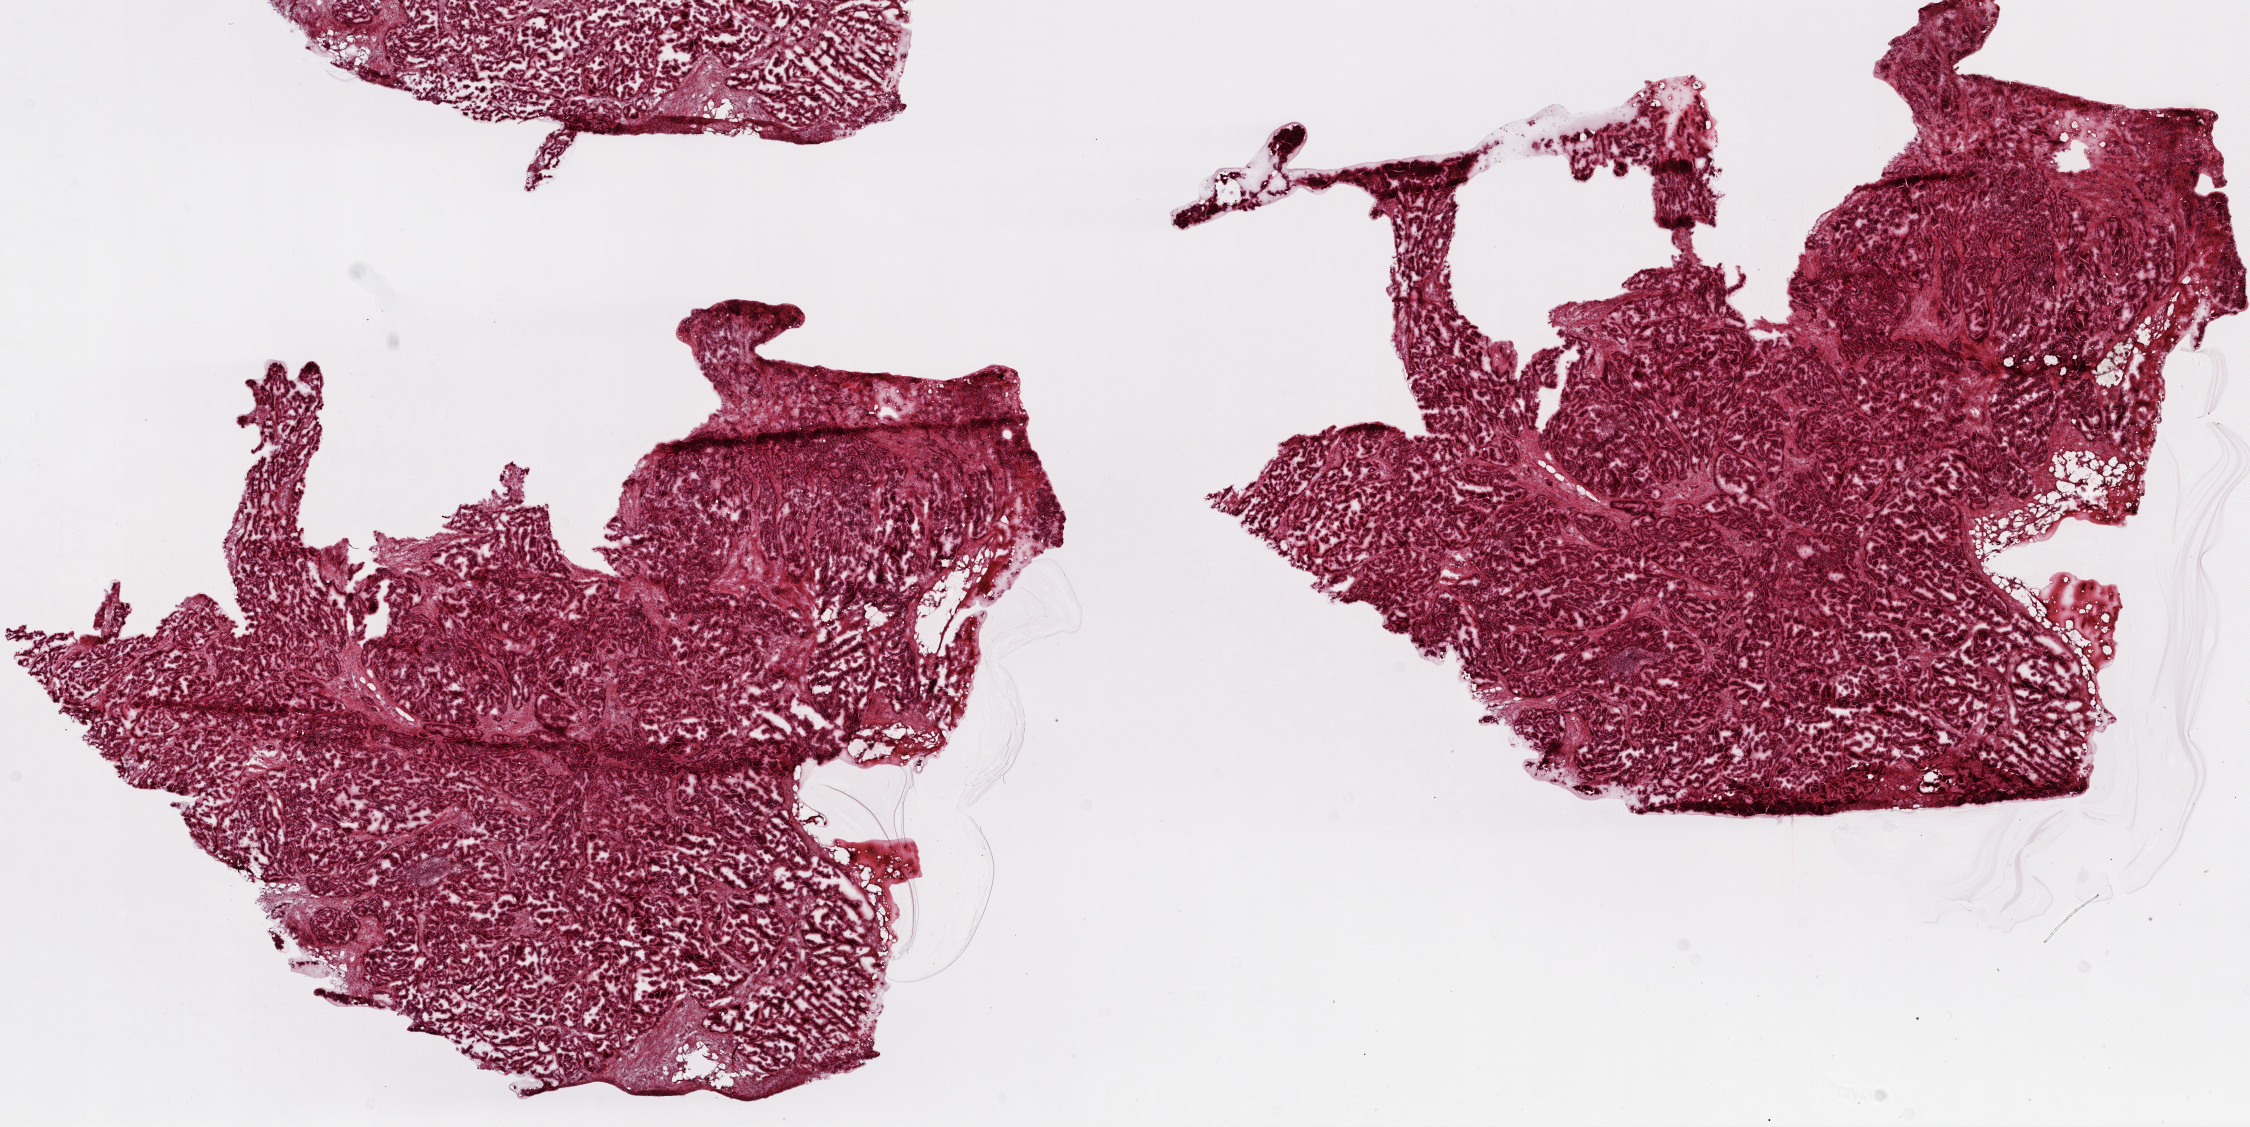
Hematoxylin and eosin (H&E) stained whole-slide image, whole scanned area (about 18.1 x 9.0 mm, from a 20x scan) shown as a low-resolution overview, frozen section from the top of the tissue portion, sample: primary tumour, ovary. Patient: female, age at initial diagnosis 57 years. Histologic grade: G3 (poorly differentiated). Composition of this section per pathologist review: tumour cells 90%, tumour nuclei 95%, normal cells 0%, stromal cells 8%, necrosis 2%.
* FIGO stage: IIIC
* diagnosis: Serous cystadenocarcinoma, NOS